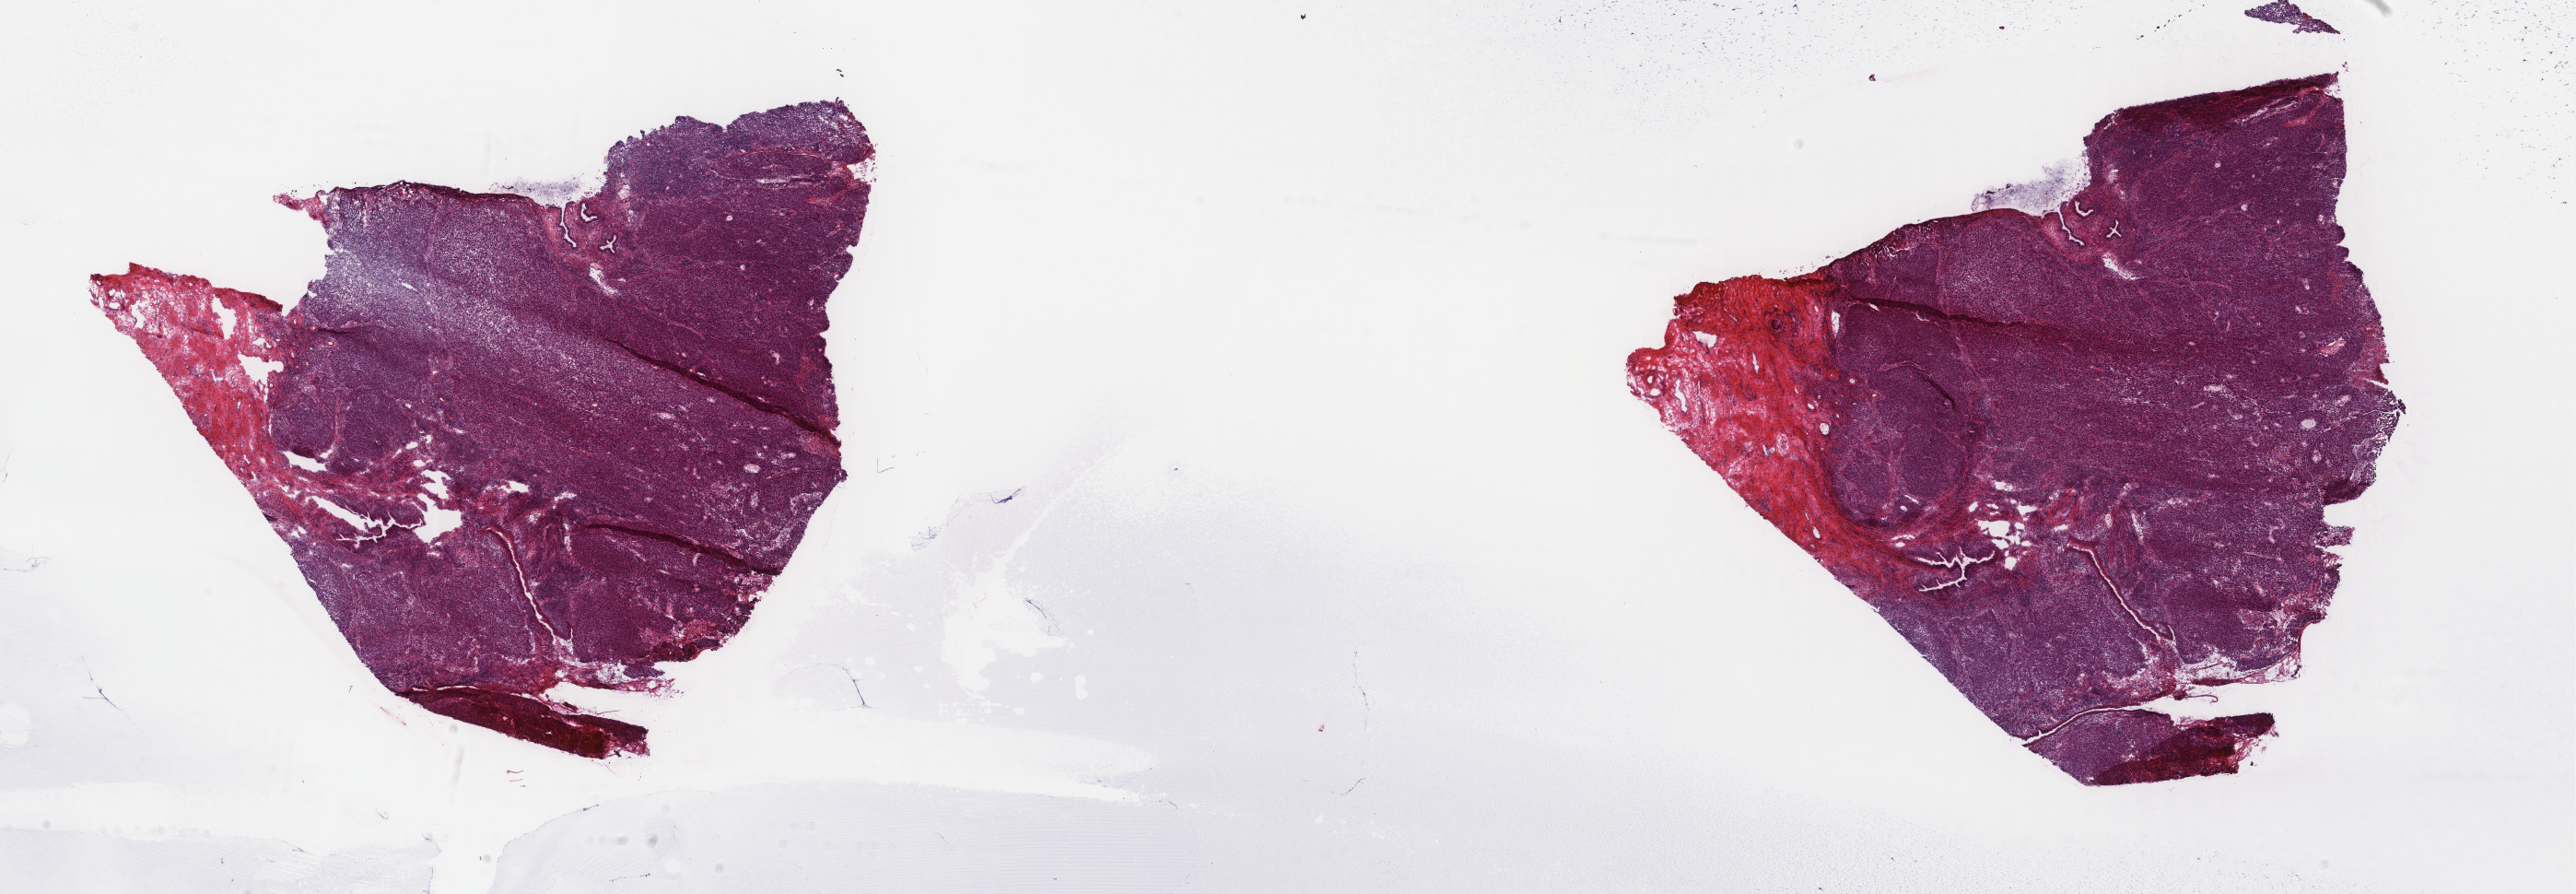
Whole-slide histology image, H&E-stained, whole scanned area (about 22.2 x 7.7 mm) shown as a low-resolution overview; frozen section from the top of the tissue portion; cervix, primary tumour sample. Patient: female, age at initial diagnosis 47 years. Histologic grade: G2 (moderately differentiated). Composition of this section per pathologist review: tumour cells 80%, tumour nuclei 80%, normal cells 0%, stromal cells 15%, necrosis 5%. Infiltration values recorded for this section: lymphocyte infiltration 40%, monocyte infiltration 5%, neutrophil infiltration 30%.
* lymph nodes positive (case pathology): 2 of 19 examined
* diagnosis: Squamous cell carcinoma, NOS
* FIGO stage: IB